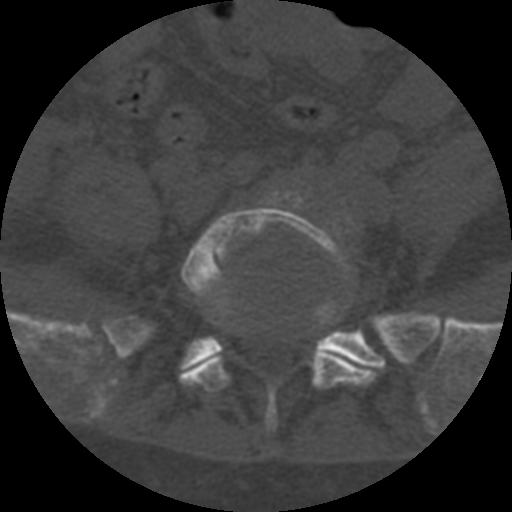
CT including the spine, one axial slice; slice 177 of 708 in the series (ordered by position); reconstruction kernel STANDARD; one of 3 acquisitions stored at this slice position; bone window (W 1800 / L 400 HU); 1.25 mm slice thickness; 512 × 512 image matrix. Patient age 55 years. From the clinical record (not read from this slice): primary cancer: colon.
Annotated regions visible in this slice (semi-automatically segmented with operator editing):
- L5 vertebra: box from (x=179, y=190) to (x=377, y=431) px